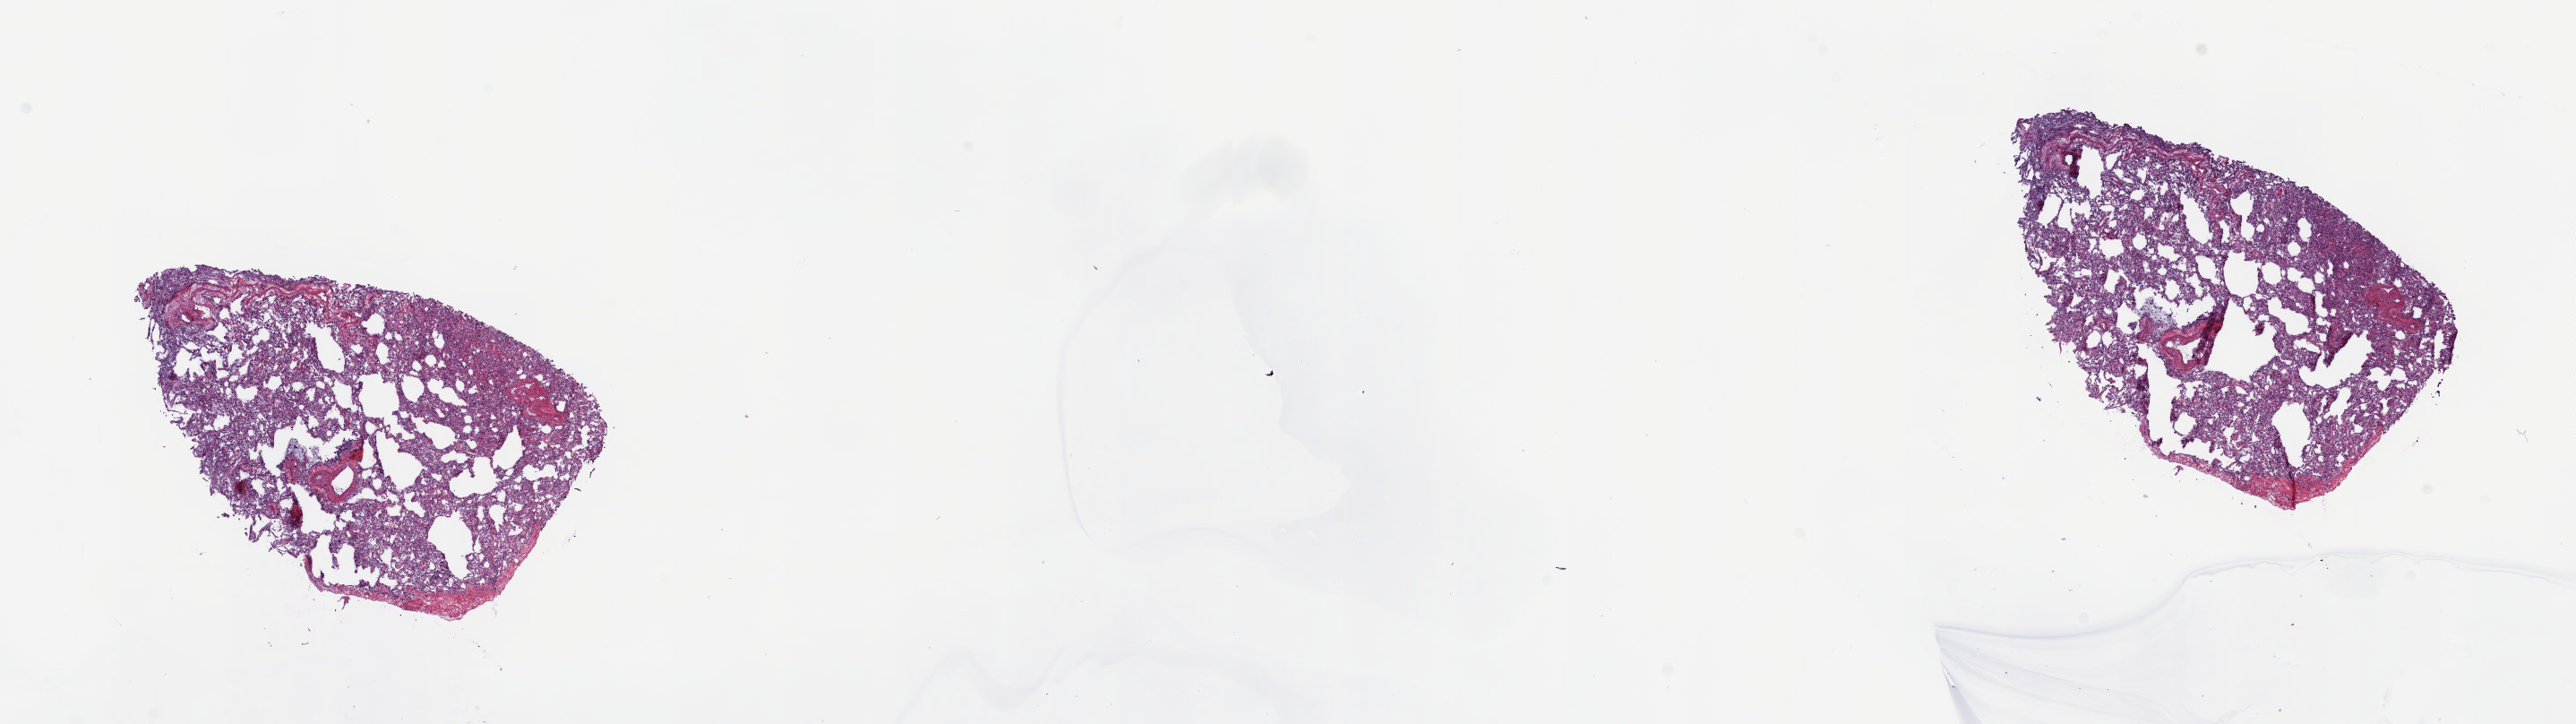
Whole-slide histology image, H&E — shown as a low-resolution overview of the whole scanned area (about 22.8 x 6.4 mm, from a 20x scan); frozen section from the top of the tissue portion; thymus, solid tissue normal (non-tumour tissue) sample. Patient: female, age at initial diagnosis 72 years. Pathologist review of this section (percent, as recorded): tumour cells 0%, tumour nuclei 0%, normal cells 100%, stromal cells 0%, necrosis 0%. Inflammatory infiltration, as recorded: lymphocyte infiltration 0%, monocyte infiltration 0%, neutrophil infiltration 0%.
* this section: solid tissue normal (non-tumour) sample from the same patient
* patient diagnosis: Thymic carcinoma, NOS (anterior mediastinum)